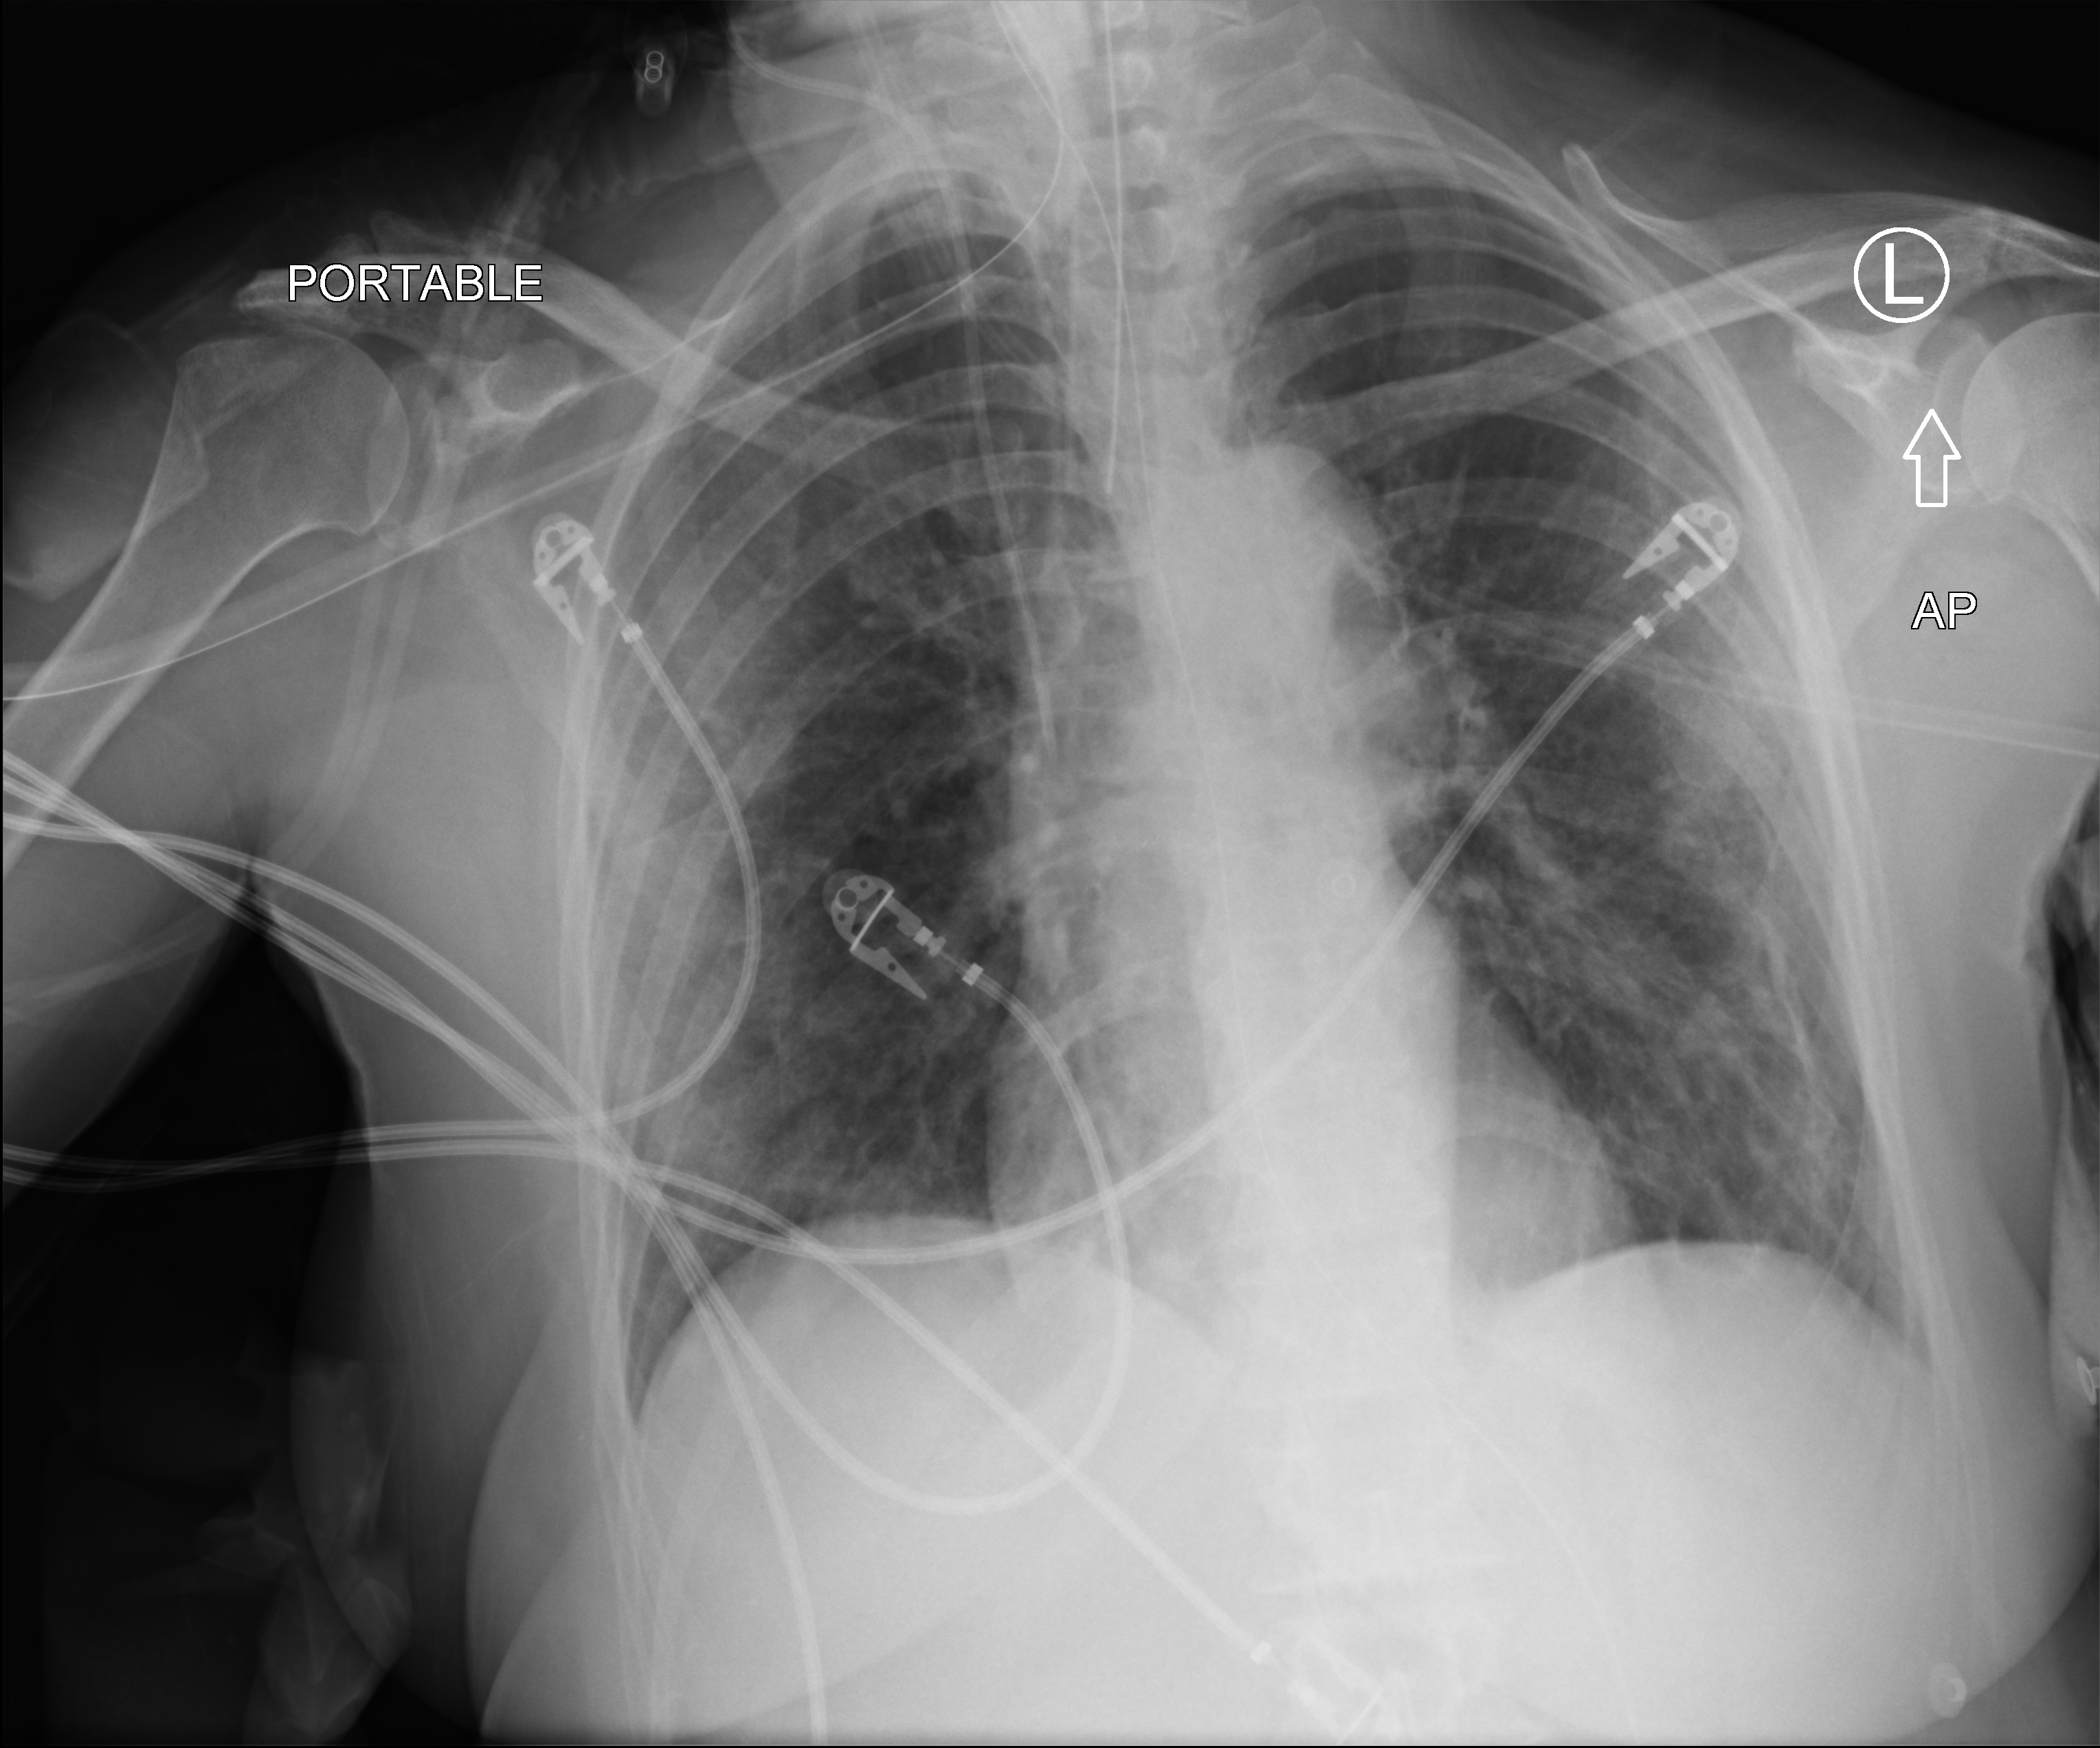
Portable chest radiograph, anteroposterior (AP) projection. Female patient hospitalised with COVID-19, age 60–74 years.
From the hospital-stay record, not from the radiograph (when in the stay this image was taken is not recorded): hypertension (admission record): yes; admitted to intensive care during this hospital stay: yes; mechanically ventilated during this hospital stay: yes.